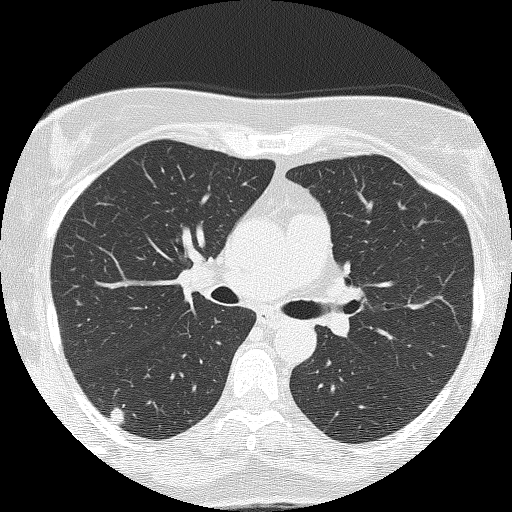
Low-dose screening chest CT, one axial slice. Position 85 of 143 along the scan axis. Lung window (W 1500 / L -600 HU). 2 mm slice thickness. 512 × 512 image matrix, field of view 301 × 301 mm.
Annotated regions visible in this slice (manually delineated by an expert):
- lesion 1 (tumor, lower lobe of right lung): box from (x=110, y=407) to (x=124, y=424) px